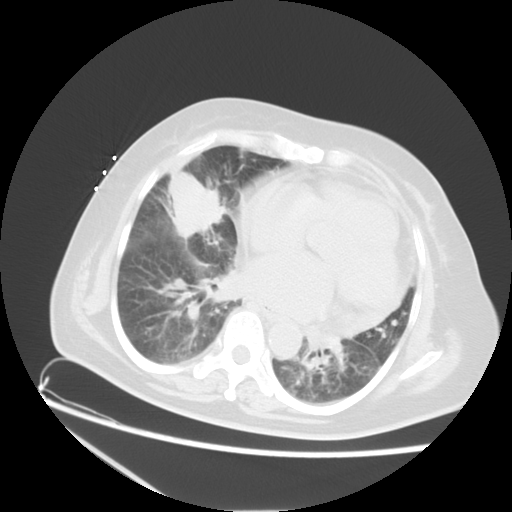
Chest CT, one axial slice. Position 8 of 22 along the scan axis. Reconstruction kernel STANDARD. Lung window (W 1500 / L -600 HU). 512 × 512 image matrix, field of view 350 × 350 mm. Female patient, age 67 years. Case-level facts recorded for this patient, not image findings: clinical TNM (as recorded): T2a N3 M1a.
Structures marked on this image (bounding box drawn by a radiologist):
- lung tumour (recorded histology: adenocarcinoma): bounding box [x1, y1, x2, y2] px = [163, 170, 229, 243]